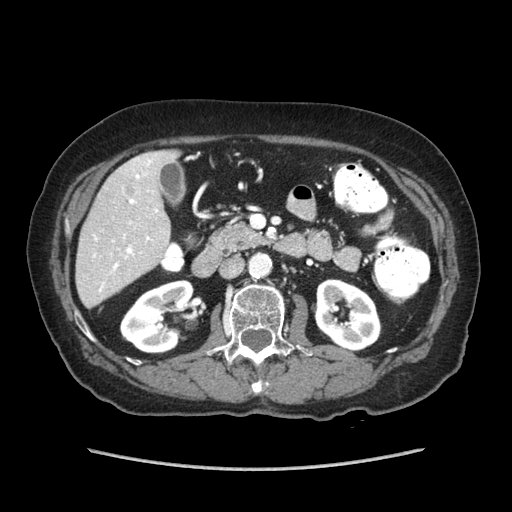
Contrast-enhanced abdominal CT (liver protocol), one axial slice. Position 26 of 89 along the scan axis. Reconstruction kernel STANDARD. Soft-tissue window (W 400 / L 40 HU). 512 × 512 image matrix. From the clinical record (not read from this slice): diagnosis: hepatocellular carcinoma (patient treated with transarterial chemoembolisation; whether this scan precedes or follows treatment is not stated here); TNM stage (as recorded): Stage-IIIA; Child-Pugh class: A; tumour differentiation: well differentiated; tumour nodularity: multinodular.
Outlined on this slice (semi-automatically segmented with operator editing):
- liver parenchyma outside the tumour (the mass and vessels are separate outlines, so this box may not span the whole liver): bounding box <76,150,178,308> (left, top, right, bottom; pixels)
- mass: <122,178,136,197>
- liver vessels: <93,159,158,291>